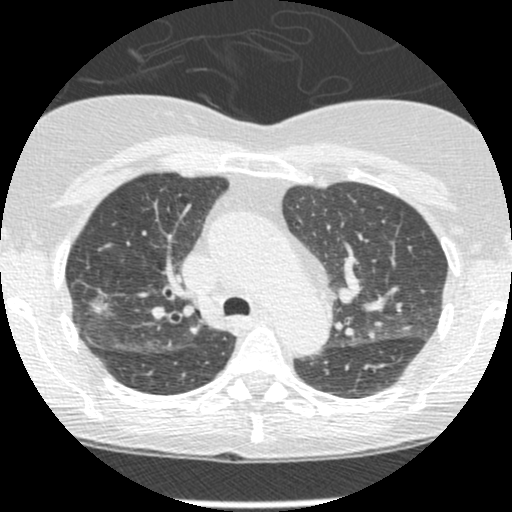
Low-dose screening chest CT, one axial slice; slice 174 of 238 in the series (ordered by position); reconstruction kernel STANDARD; 120 kVp; lung window (W 1500 / L -600 HU); 1.25 mm slice thickness; 512 × 512 image matrix, field of view 288 × 288 mm.
Structures marked on this image (outlined manually by an expert reader):
- lesion 1 (tumor, upper lobe of right lung): bounding box <91,296,109,315> (left, top, right, bottom; pixels)